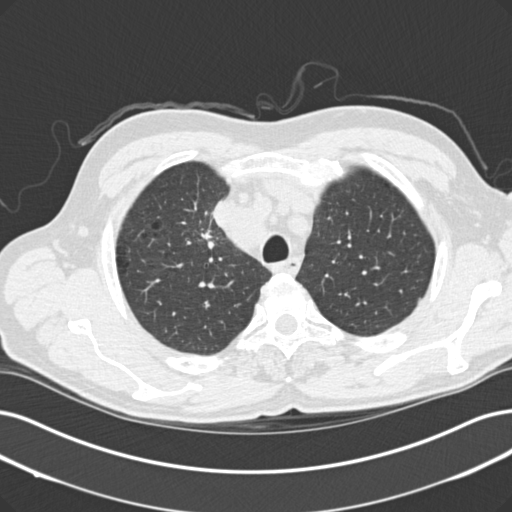
Low-dose screening chest CT, one axial slice. Reconstruction kernel B30f. 120 kVp. Lung window (W 1500 / L -600 HU). 2 mm slice thickness. 512 × 512 image matrix, field of view 365 × 365 mm.
Outlined on this slice (outlined manually by an expert reader):
- lesion 1 (tumor, upper lobe of right lung): bounding box [x1, y1, x2, y2] px = [201, 229, 212, 240]